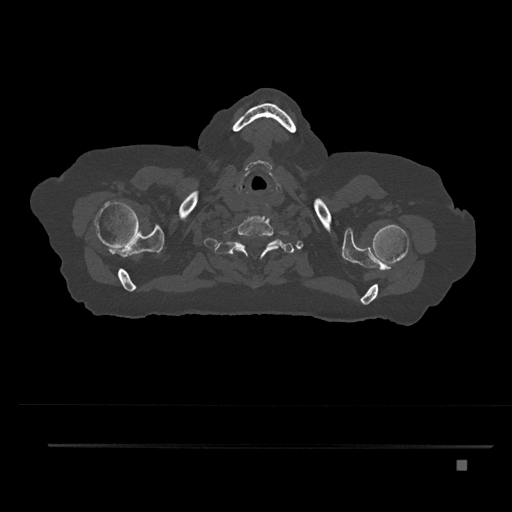
CT including the spine, one axial slice; position 714 of 797 along the scan axis; reconstruction kernel Br40s/3; bone window (W 1800 / L 400 HU); 0.5 mm slice thickness; 512 × 512 image matrix, field of view 437 × 437 mm. Patient: female, 76 years. Case-level facts recorded for this patient, not image findings: primary cancer: lung.
Outlined on this slice (semi-automatically segmented with operator editing):
- T1 vertebra: box from (x=223, y=243) to (x=283, y=257) px